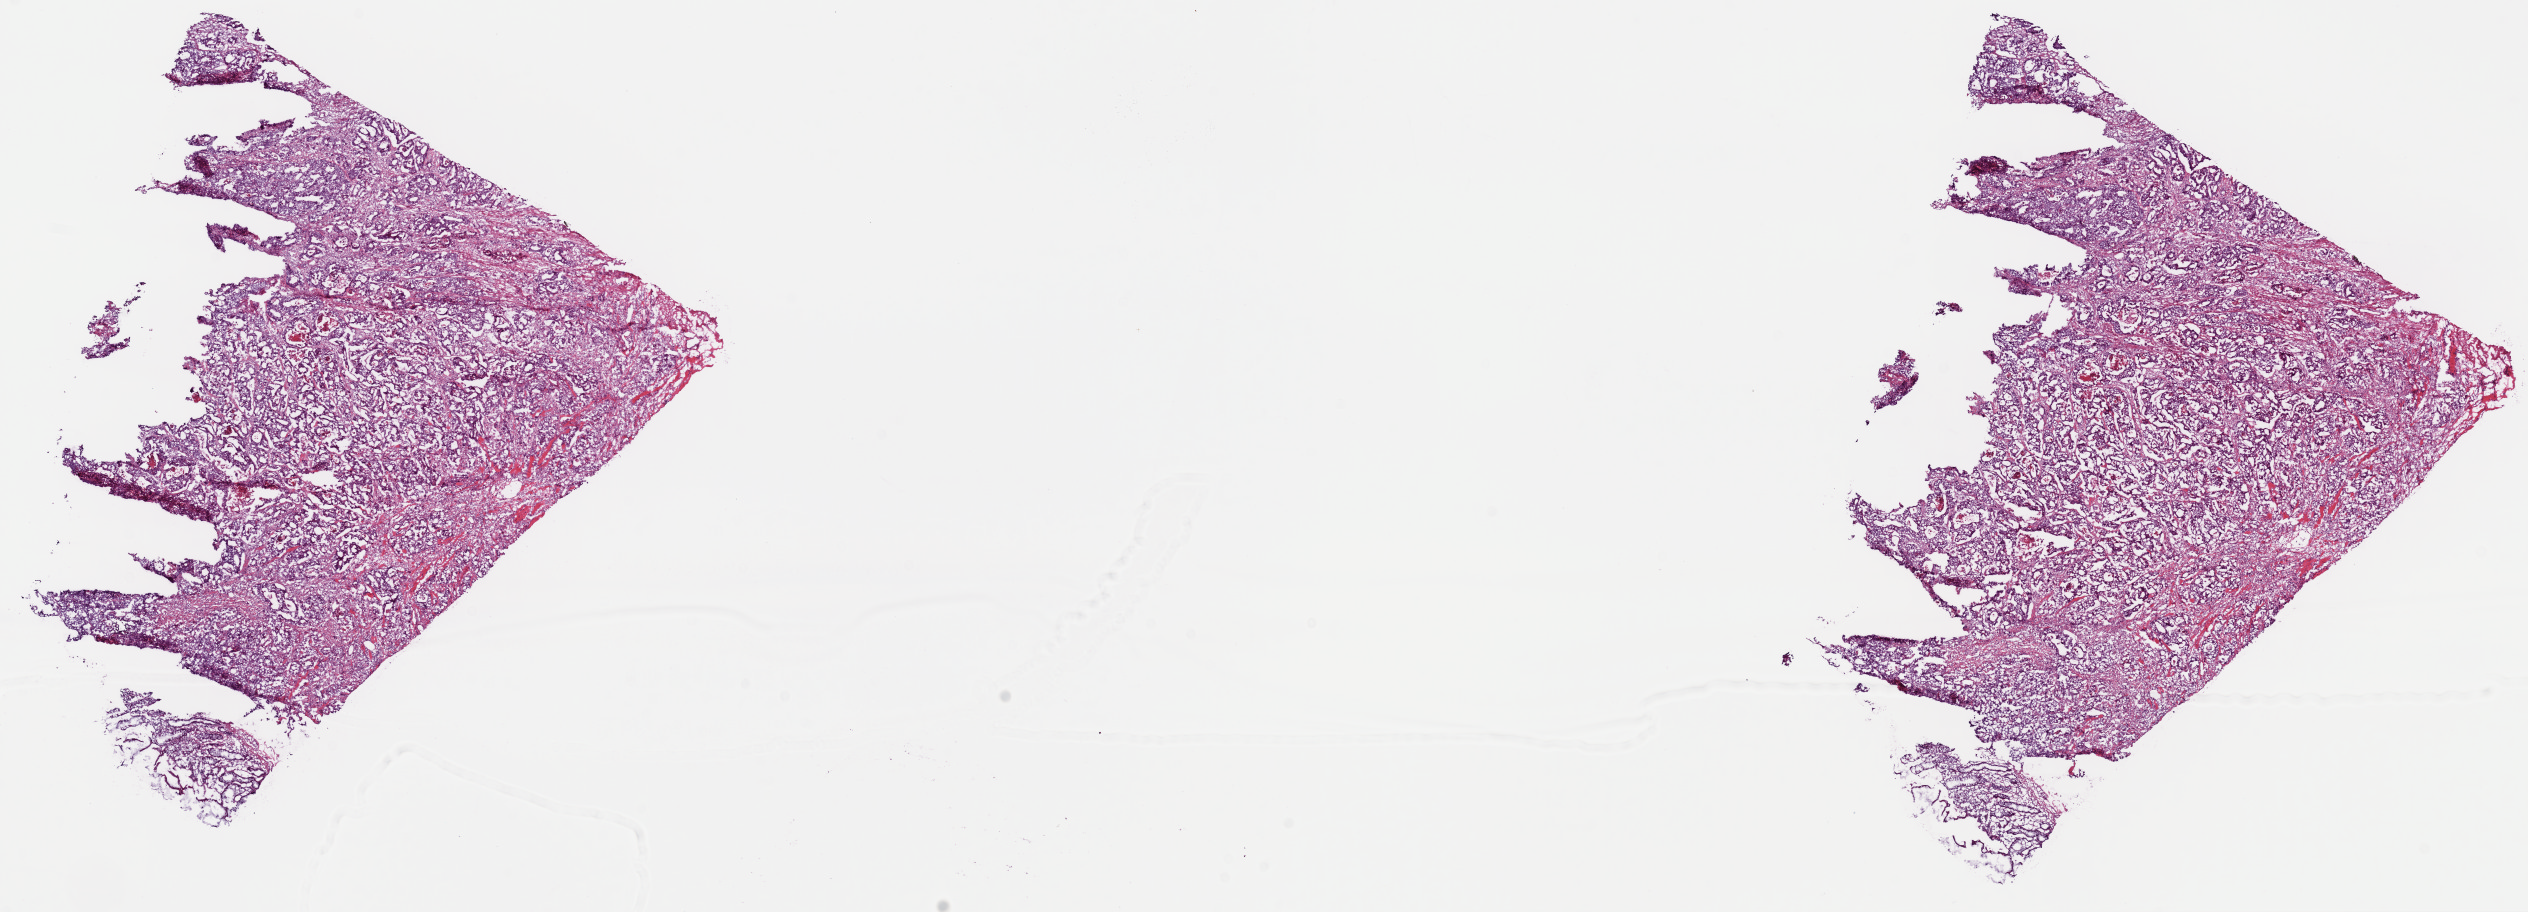
Whole-slide histology image, H&E-stained — low-resolution overview of the scanned area, about 20.0 x 7.2 mm (acquisition: 40x scan), frozen section from the top of the tissue portion, sample: primary tumour, colon. Male, age 78 years at initial diagnosis. Composition of this section per pathologist review: tumour cells 80%, tumour nuclei 80%, normal cells 5%, stromal cells 13%, necrosis 2%. Infiltration values recorded for this section: lymphocyte infiltration 2%, monocyte infiltration 1%, neutrophil infiltration 2%.
AJCC pathologic stage: IIIC (6th edition). Lymph nodes positive (case pathology): 6 of 15 examined. TNM: T3 N2 M0. Histologic diagnosis: Adenocarcinoma, NOS (cecum).